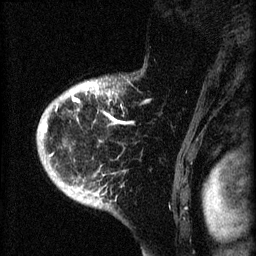
Breast MRI (dynamic contrast-enhanced), one sagittal slice; slice 54 of 60 in the series (ordered by position); dynamic contrast-enhanced series, image 2 of 4 at this slice position (ordered by acquisition); 1.5 T; TE 4.2 ms, TR 8.2 ms; 2 mm slice thickness; 256 × 256 image matrix. Patient: female, 71 years.
Outlined on this slice (semi-automatic segmentation, software-assisted and operator-edited):
- analysis volume of interest (the breast-tissue region the enhancement analysis was run in; not a lesion): bounding box (x1, y1, x2, y2) in pixels: (37, 76, 142, 190)
- tumour enhancement mask (voxels above the 70 % enhancement threshold inside the analysis volume of interest): (42, 81, 115, 156)